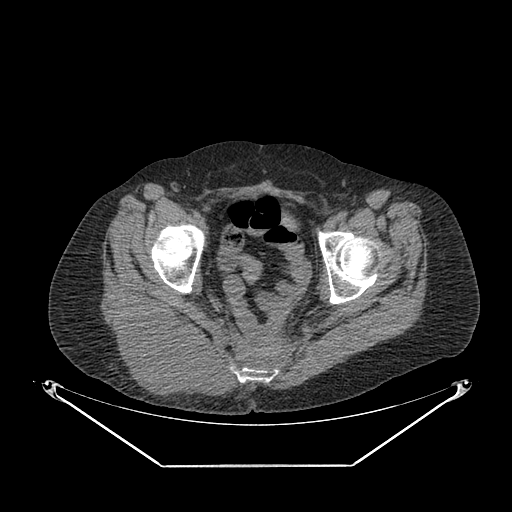
CT of an extremity soft-tissue mass (from a PET/CT study), one axial slice; slice 58 of 267 in the series (ordered by position); reconstruction kernel SOFT; 140 kVp; soft-tissue window (W 400 / L 40 HU); 3.75 mm slice thickness; 512 × 512 image matrix, field of view 500 × 500 mm. Female patient. Case-level facts recorded for this patient, not image findings: histological type: spindle cell suggestive of myxofibrosarcoma; grade: intermediate; site of the primary tumour: right buttock.
Annotated regions visible in this slice (expert contour drawn on MRI and transferred to this co-registered scan by the dataset authors):
- gross tumour volume (mass): bounding box (x1, y1, x2, y2) in pixels: (110, 306, 223, 403)